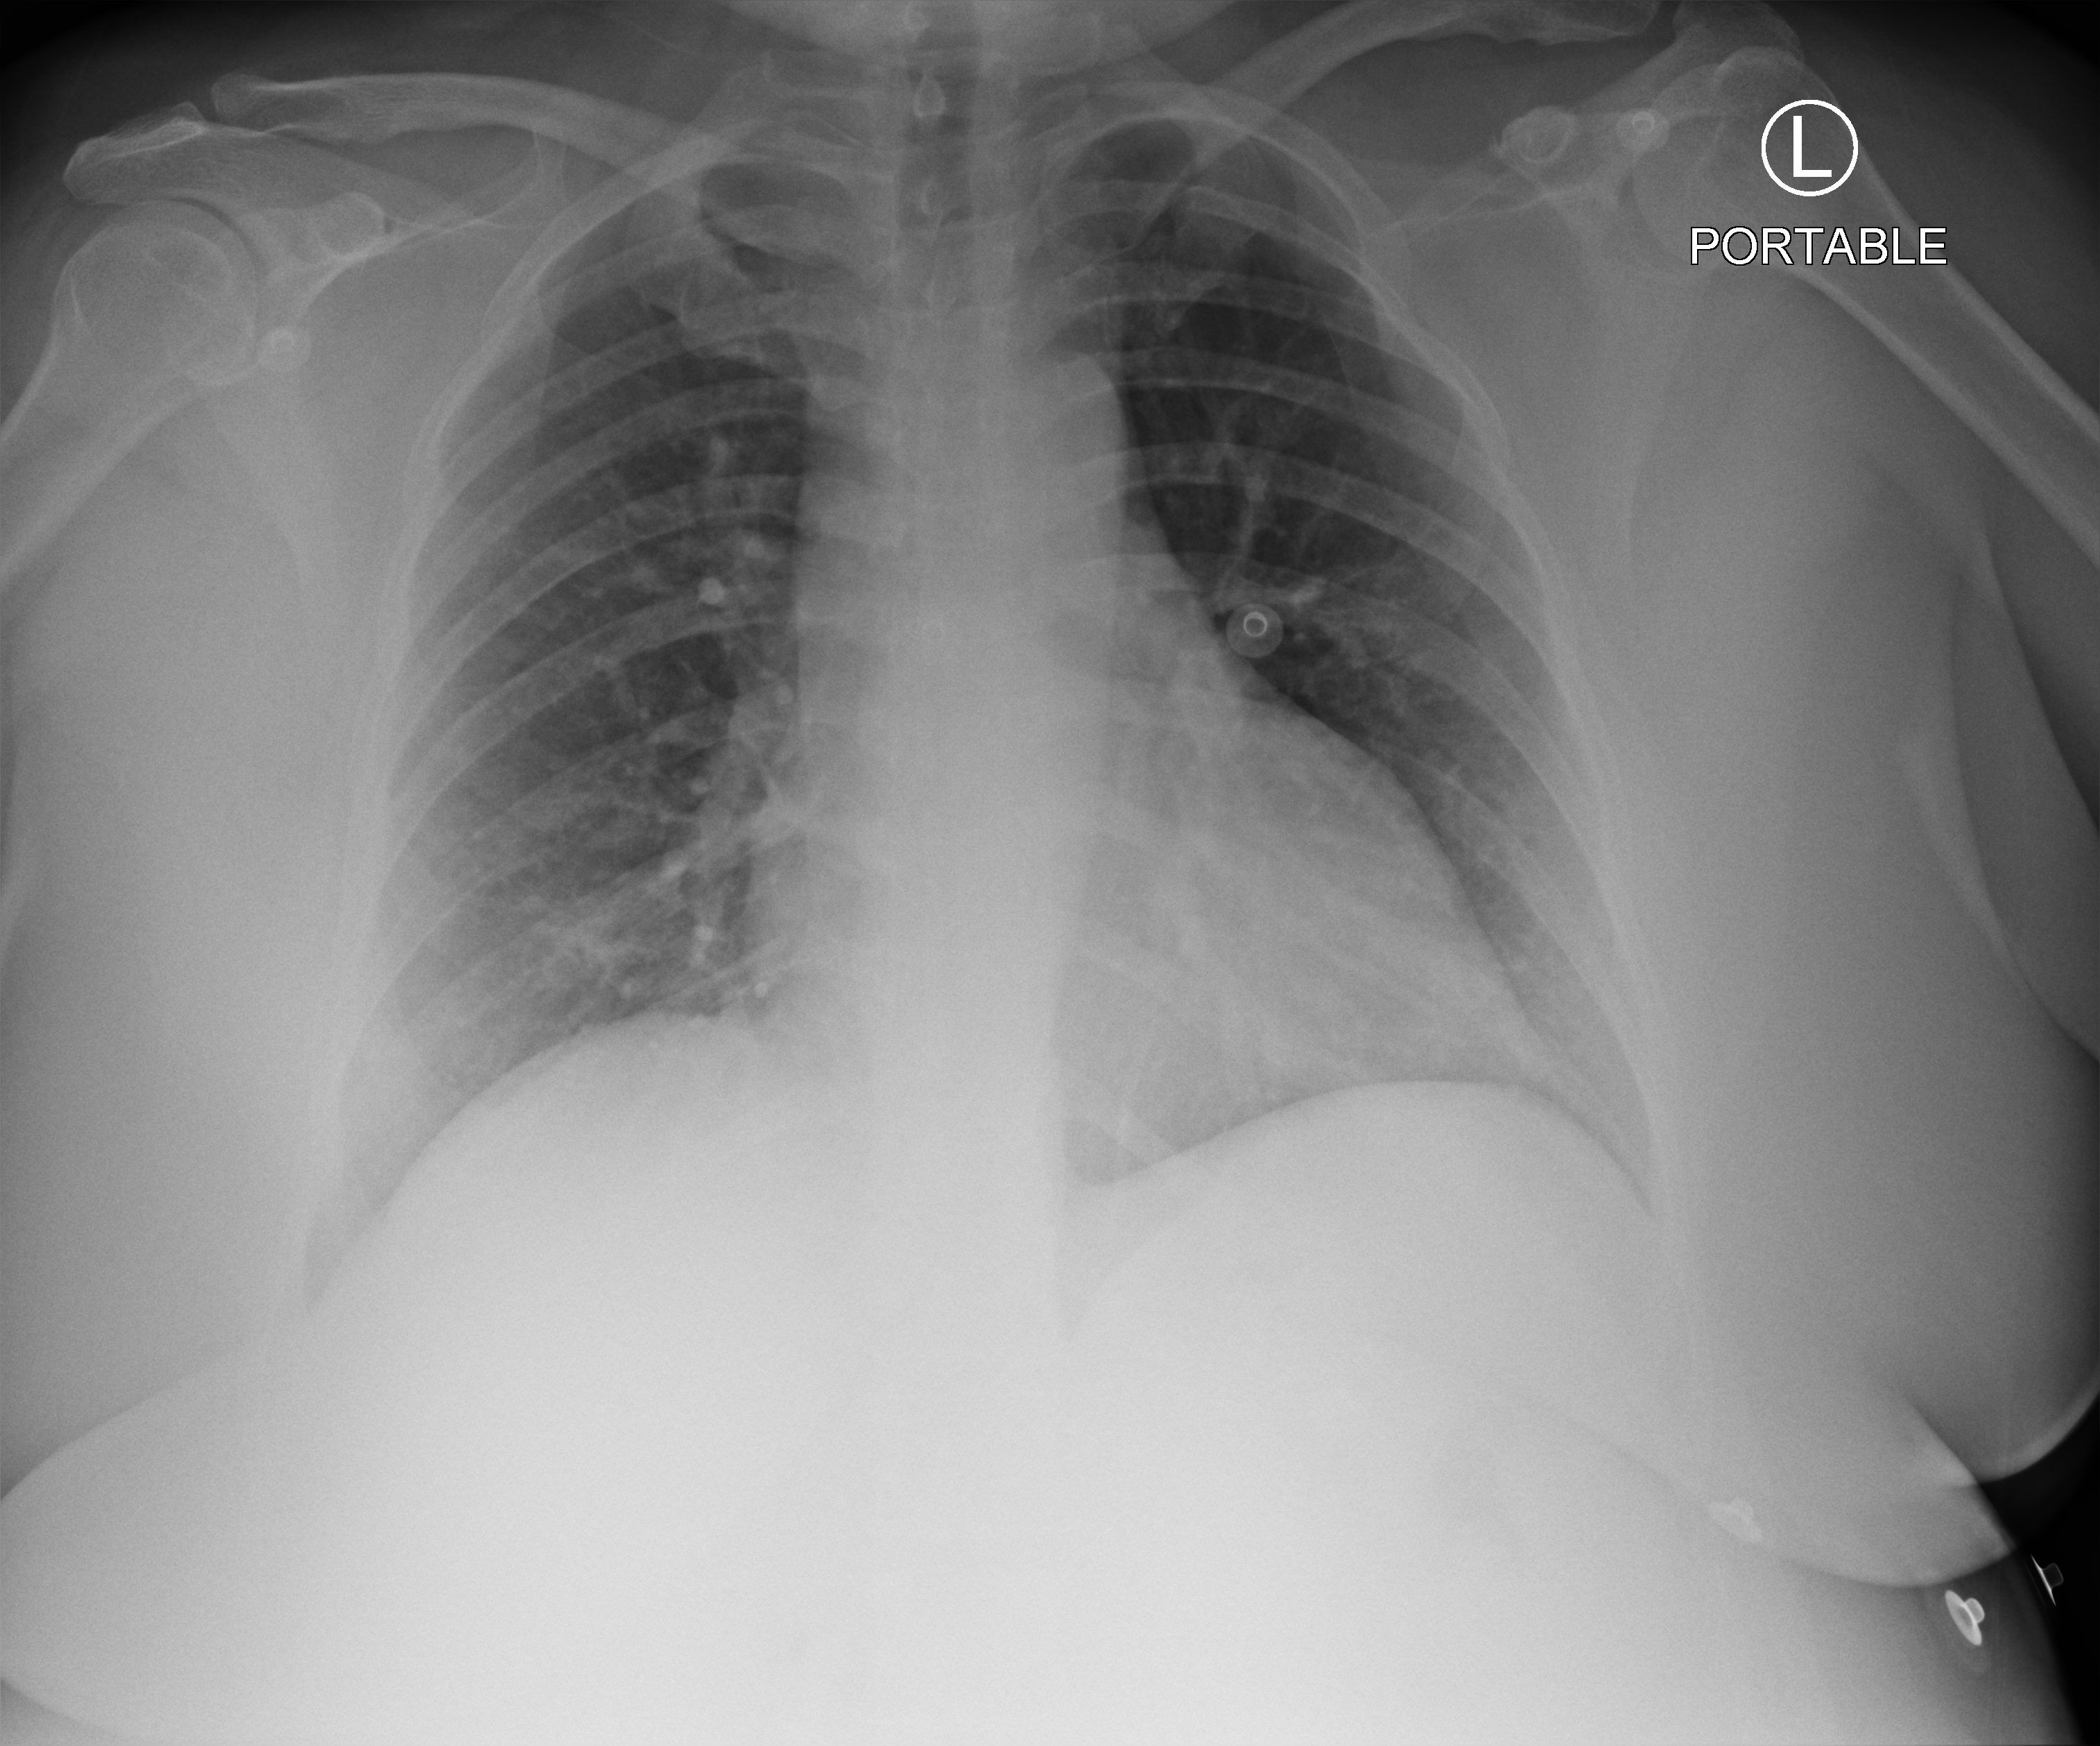
Portable chest radiograph; anteroposterior (AP) projection. Female patient hospitalised with COVID-19, age 18–59 years.
From the hospital-stay record, not from the radiograph (when in the stay this image was taken is not recorded):
- mechanically ventilated during this hospital stay: no